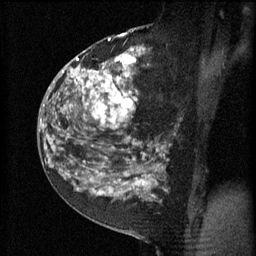
Breast MRI (dynamic contrast-enhanced), one sagittal slice. Position 30 of 60 along the scan axis. 3 images stored at this slice position (order not interpretable as contrast timing). 1.5 T. TE 4.2 ms, TR 11 ms. 256 × 256 image matrix. Patient: female, 52 years.
Outlined on this slice (semi-automatic segmentation, software-assisted and operator-edited):
- analysis volume of interest (the breast-tissue region the enhancement analysis was run in; not a lesion): box from (x=81, y=52) to (x=165, y=157) px
- tumour enhancement mask (voxels above the 70 % enhancement threshold inside the analysis volume of interest): (x=81, y=54)–(x=159, y=151)